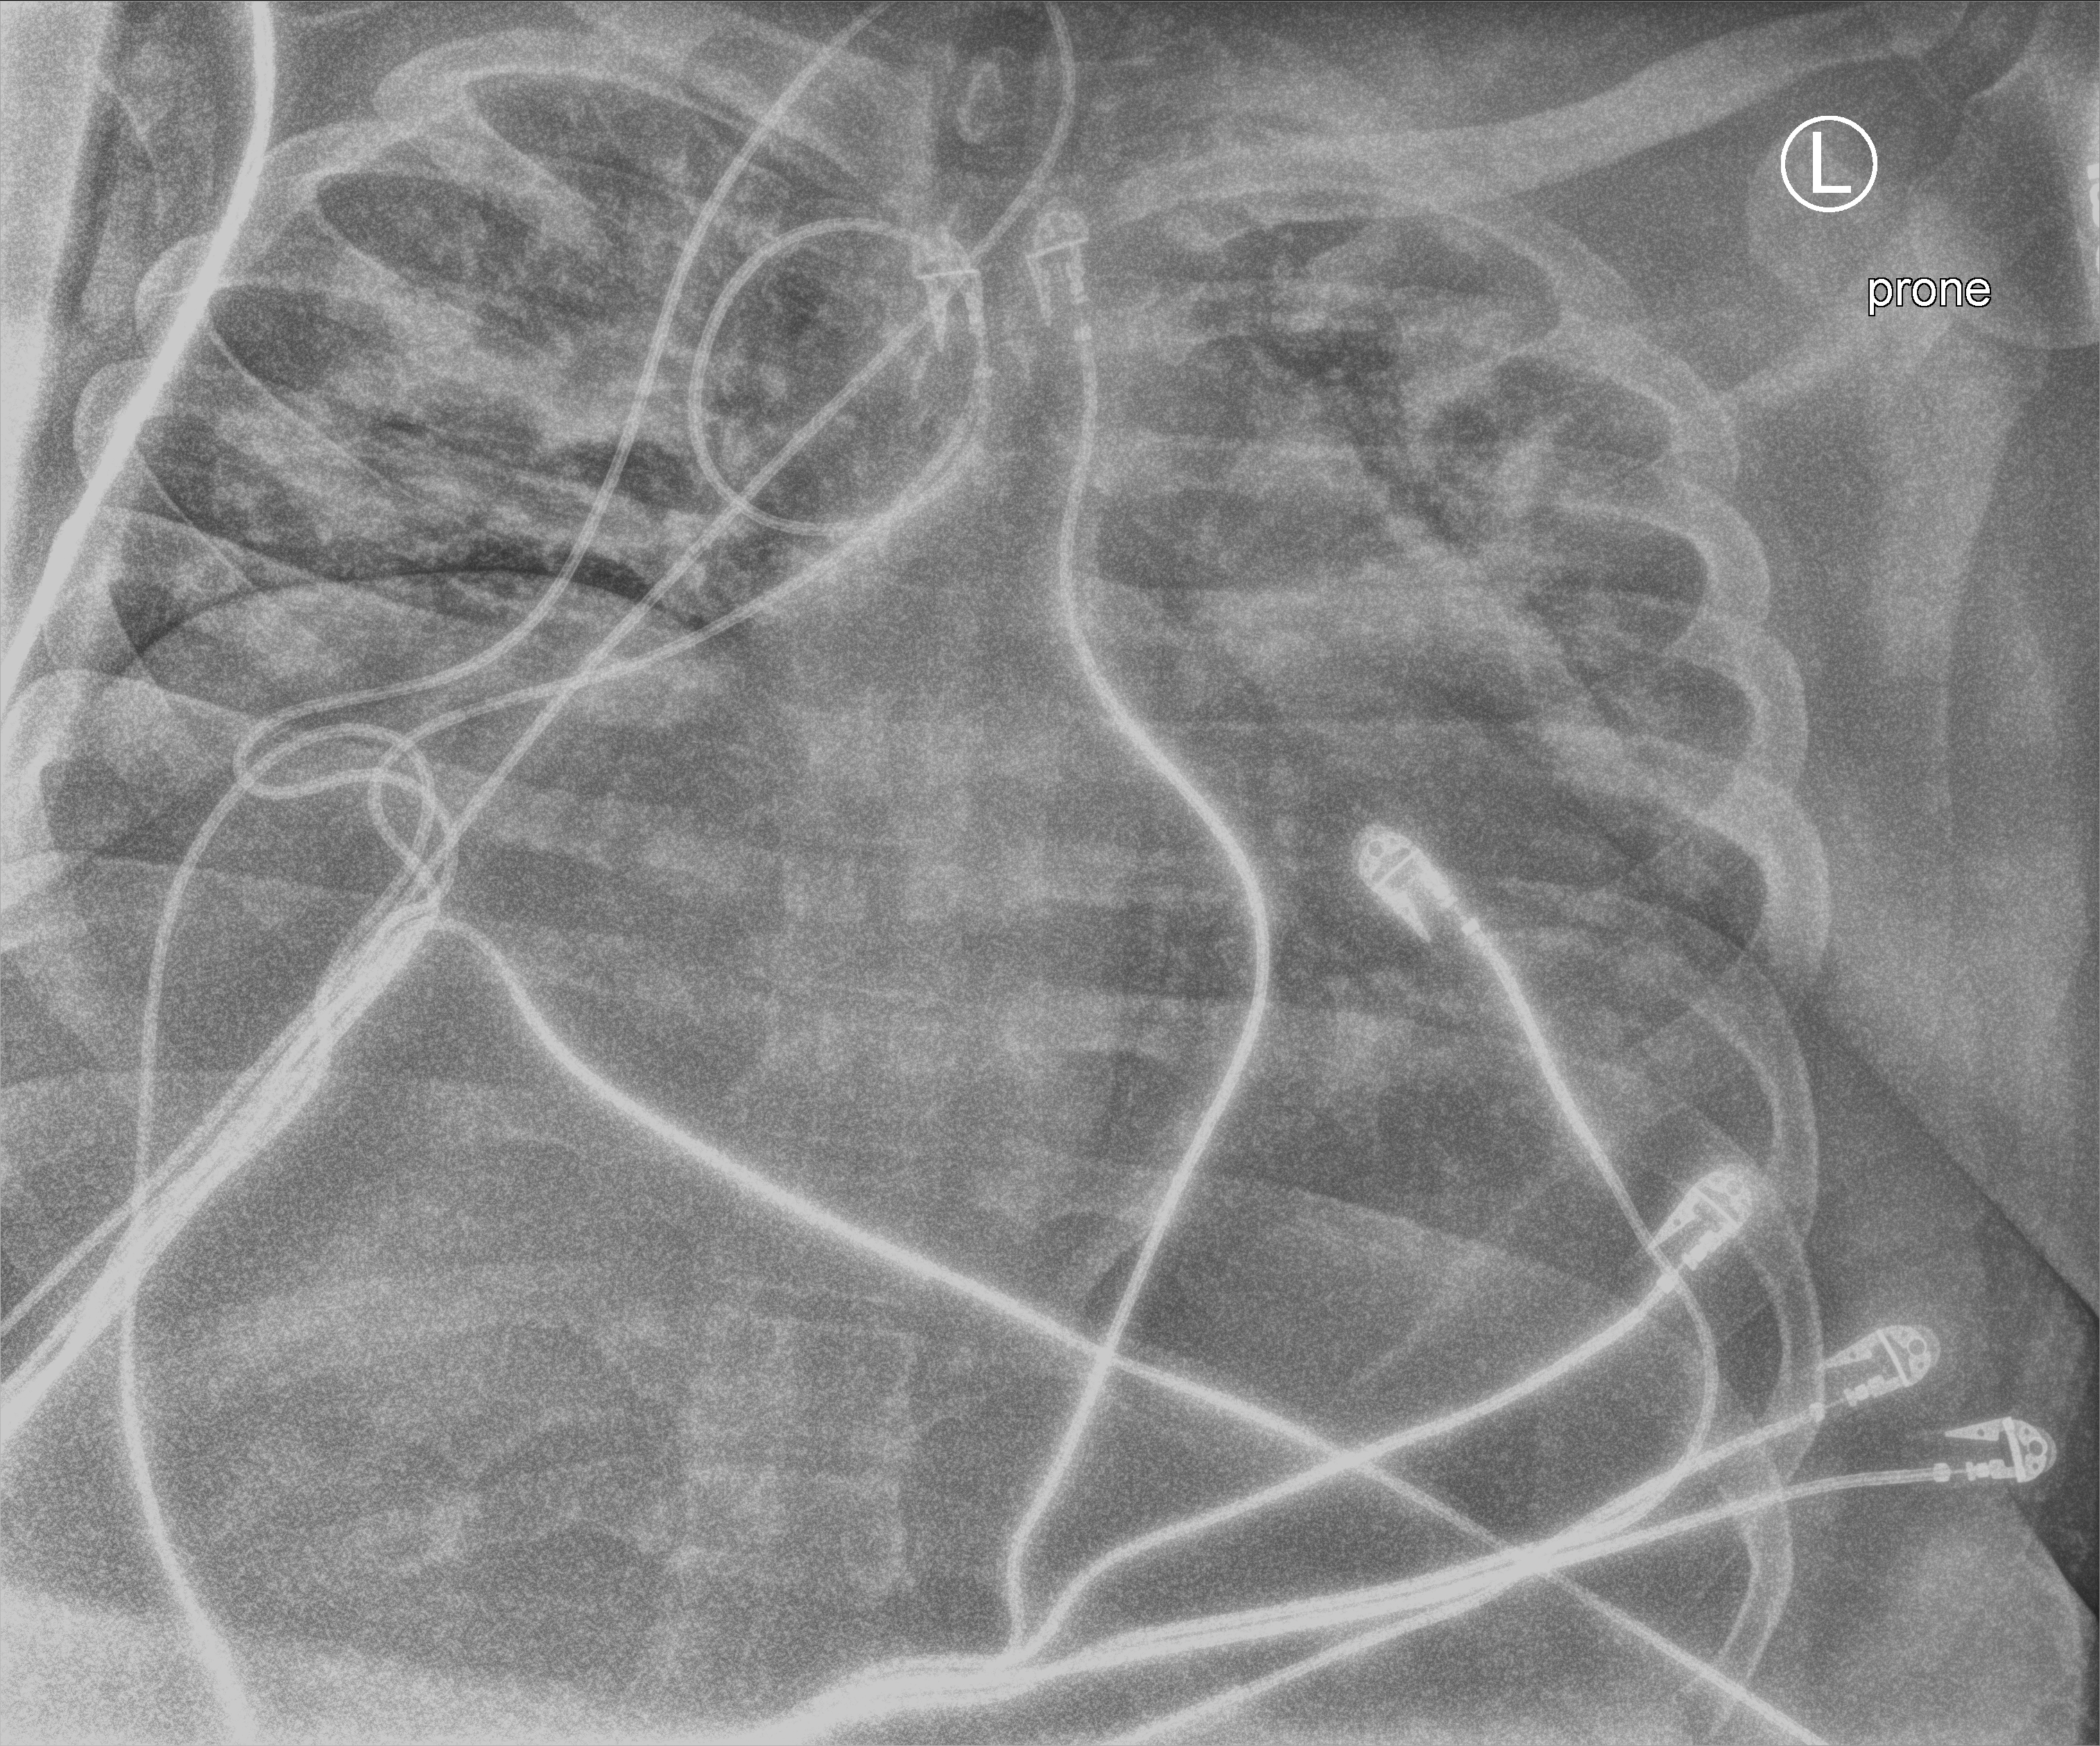
Chest X-ray (portable), anteroposterior (AP) projection. Male patient hospitalised with COVID-19, age 18–59 years.
From the hospital-stay record, not from the radiograph (when in the stay this image was taken is not recorded): smoking status (admission record): never; mechanically ventilated during this hospital stay: yes; other chronic lung disease (admission record): yes.